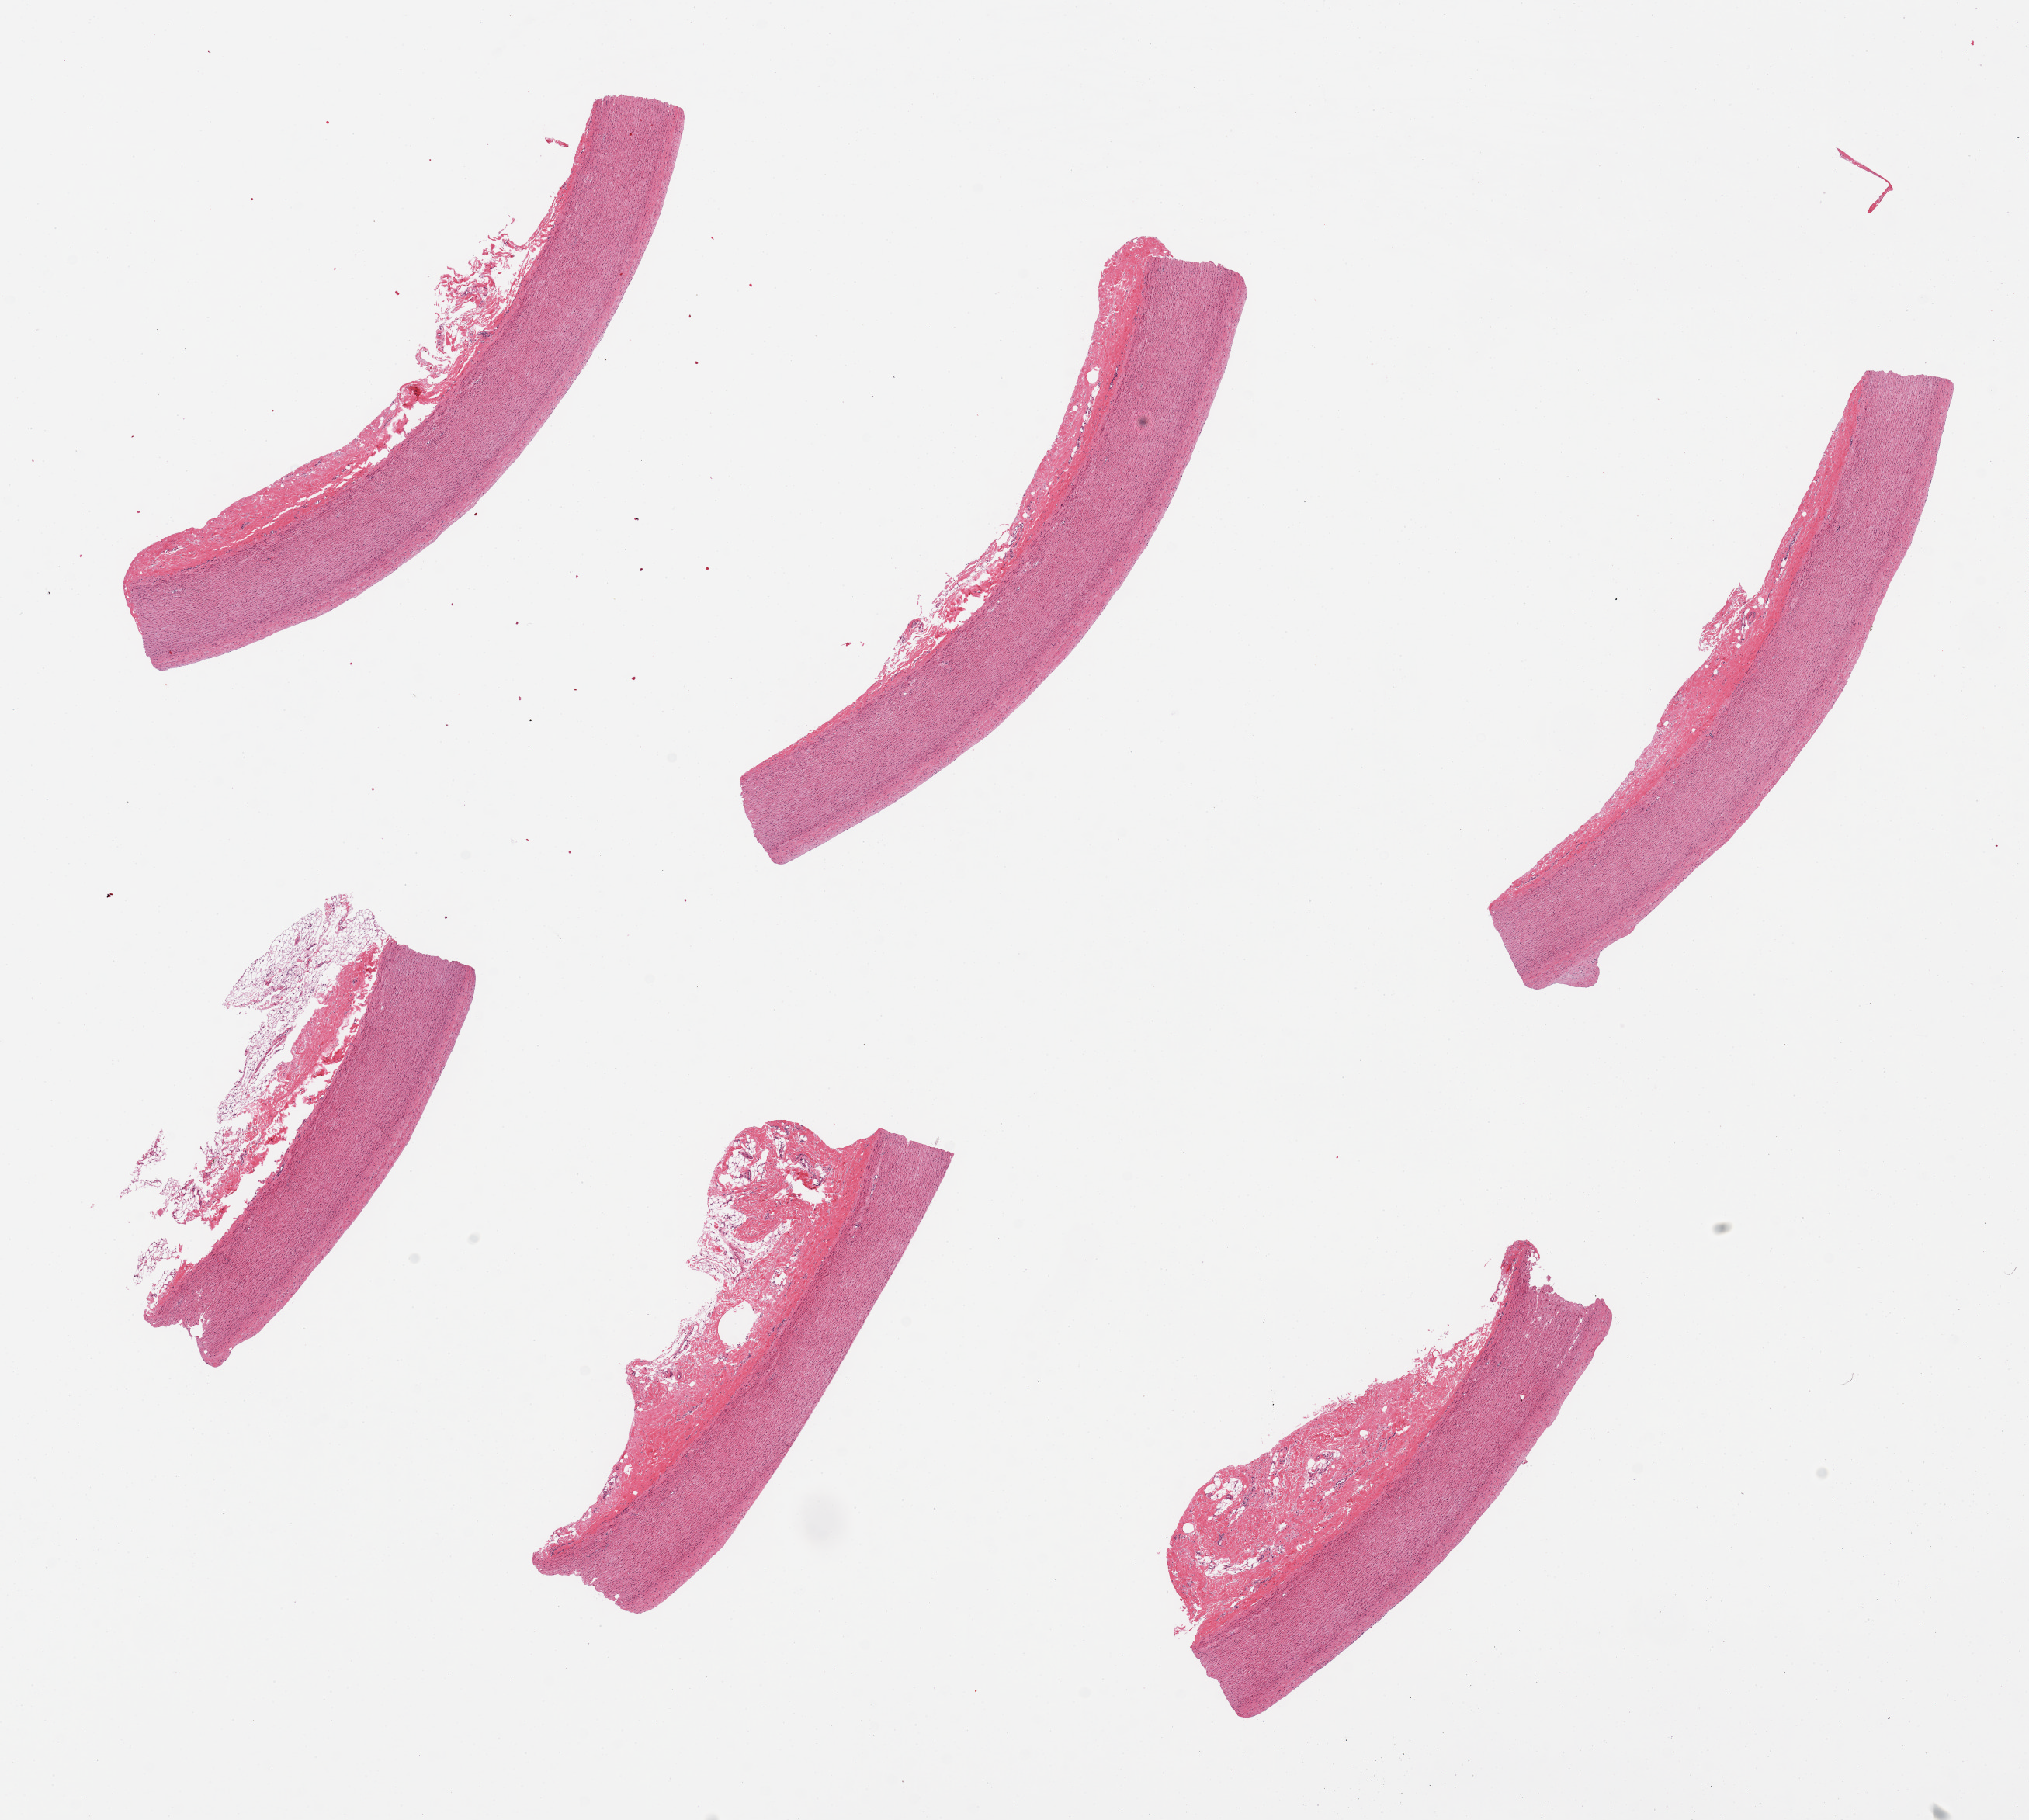
Digitized haematoxylin and eosin-stained section, whole scanned area (about 20.7 x 18.5 mm, acquisition: 20x scan) shown as a low-resolution overview; PAXgene-fixed paraffin-embedded (PFPE) section; target tissue: aorta; donor tissue sample. Female donor.
• review note (as recorded): 6 pieces, some attached adventitia/fat